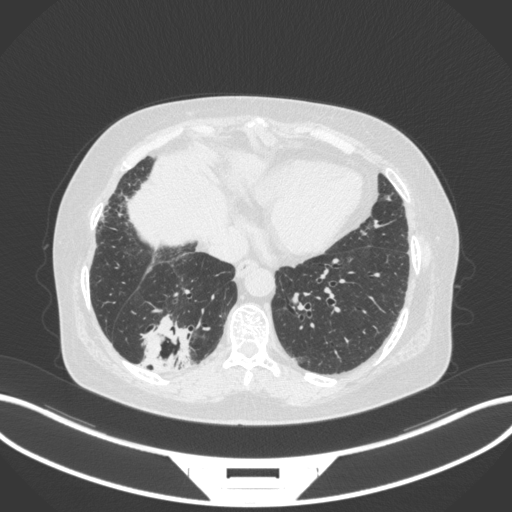
Chest CT, one axial slice. Position 57 of 303 along the scan axis. Reconstruction kernel B31f. 120 kVp. Lung window (W 1500 / L -600 HU). 1 mm slice thickness. 512 × 512 image matrix, field of view 400 × 400 mm. Female patient, age 65 years. Case-level facts recorded for this patient, not image findings: clinical TNM (as recorded): T2b N1 M0; histopathological grade: G1.
Outlined on this slice (rectangle marked by the reading radiologist):
- lung tumour (recorded histology: adenocarcinoma): bounding box [x1, y1, x2, y2] px = [135, 313, 196, 373]